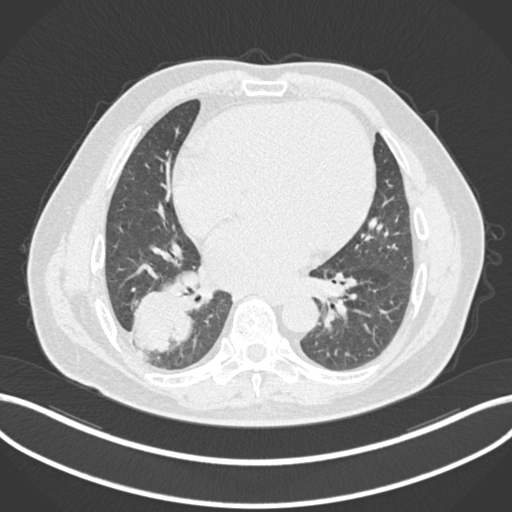
Chest CT, one axial slice. Position 72 of 200 along the scan axis. Lung window (W 1500 / L -600 HU). 1 mm slice thickness. 512 × 512 image matrix, field of view 400 × 400 mm. Patient: male, 59 years.
Outlined on this slice (bounding box drawn by a radiologist):
- lung tumour (recorded histology: adenocarcinoma): bounding box [x1, y1, x2, y2] px = [130, 285, 196, 358]